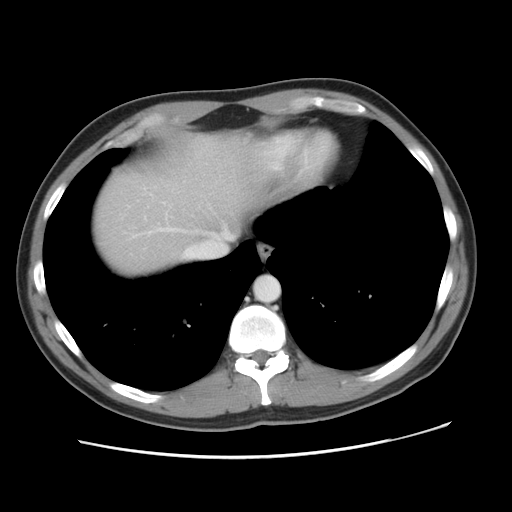
Contrast-enhanced abdominal CT, one axial slice. Position 43 of 49 along the scan axis. 120 kVp. Intravenous contrast given. Soft-tissue window (W 400 / L 40 HU). 512 × 512 image matrix. Male patient, age 41 years. From the clinical record (not read from this slice): diagnosis: colorectal cancer liver metastases, imaged before liver resection; multiple liver metastases: yes; largest metastasis: 0.7 cm; disease in both lobes: yes.
Outlined on this slice (manually delineated by an expert):
- hepatic veins: box from (x=126, y=205) to (x=233, y=257) px
- liver: (x=92, y=137)–(x=253, y=276)
- planned liver remnant (the part of the liver to remain after resection): (x=115, y=137)–(x=254, y=241)